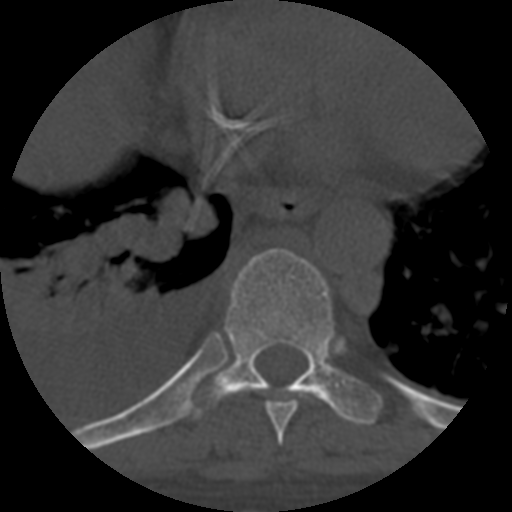
CT including the spine, one axial slice. Slice 383 of 708 in the series (ordered by position). Reconstruction kernel STANDARD. 120 kVp. One of 3 acquisitions stored at this slice position. Bone window (W 1800 / L 400 HU). 1.25 mm slice thickness. 512 × 512 image matrix, field of view 160 × 160 mm. Patient age 55 years. Case-level facts recorded for this patient, not image findings: primary cancer: colon.
Outlined on this slice (semi-automatic segmentation, software-assisted and operator-edited):
- T8 vertebra: bounding box [x1, y1, x2, y2] px = [265, 397, 302, 445]
- T9 vertebra: [192, 248, 380, 426]